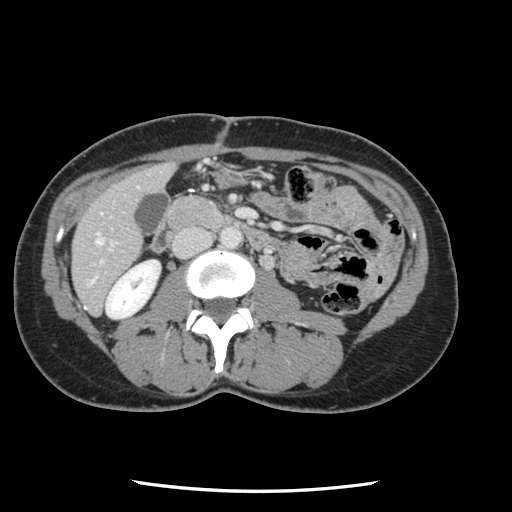
Contrast-enhanced abdominal CT, one axial slice; position 27 of 134 along the scan axis; 120 kVp; intravenous contrast given; soft-tissue window (W 400 / L 40 HU); 2.5 mm slice thickness; 512 × 512 image matrix, field of view 330 × 330 mm. Female patient, age 43 years. Case-level facts recorded for this patient, not image findings: diagnosis: colorectal cancer liver metastases, imaged before liver resection; multiple liver metastases: yes; largest metastasis: 3.4 cm.
Annotated regions visible in this slice (manually delineated by an expert):
- hepatic veins: box from (x=96, y=236) to (x=102, y=245) px
- liver: (x=73, y=165)–(x=173, y=314)
- planned liver remnant (the part of the liver to remain after resection): (x=73, y=165)–(x=173, y=314)